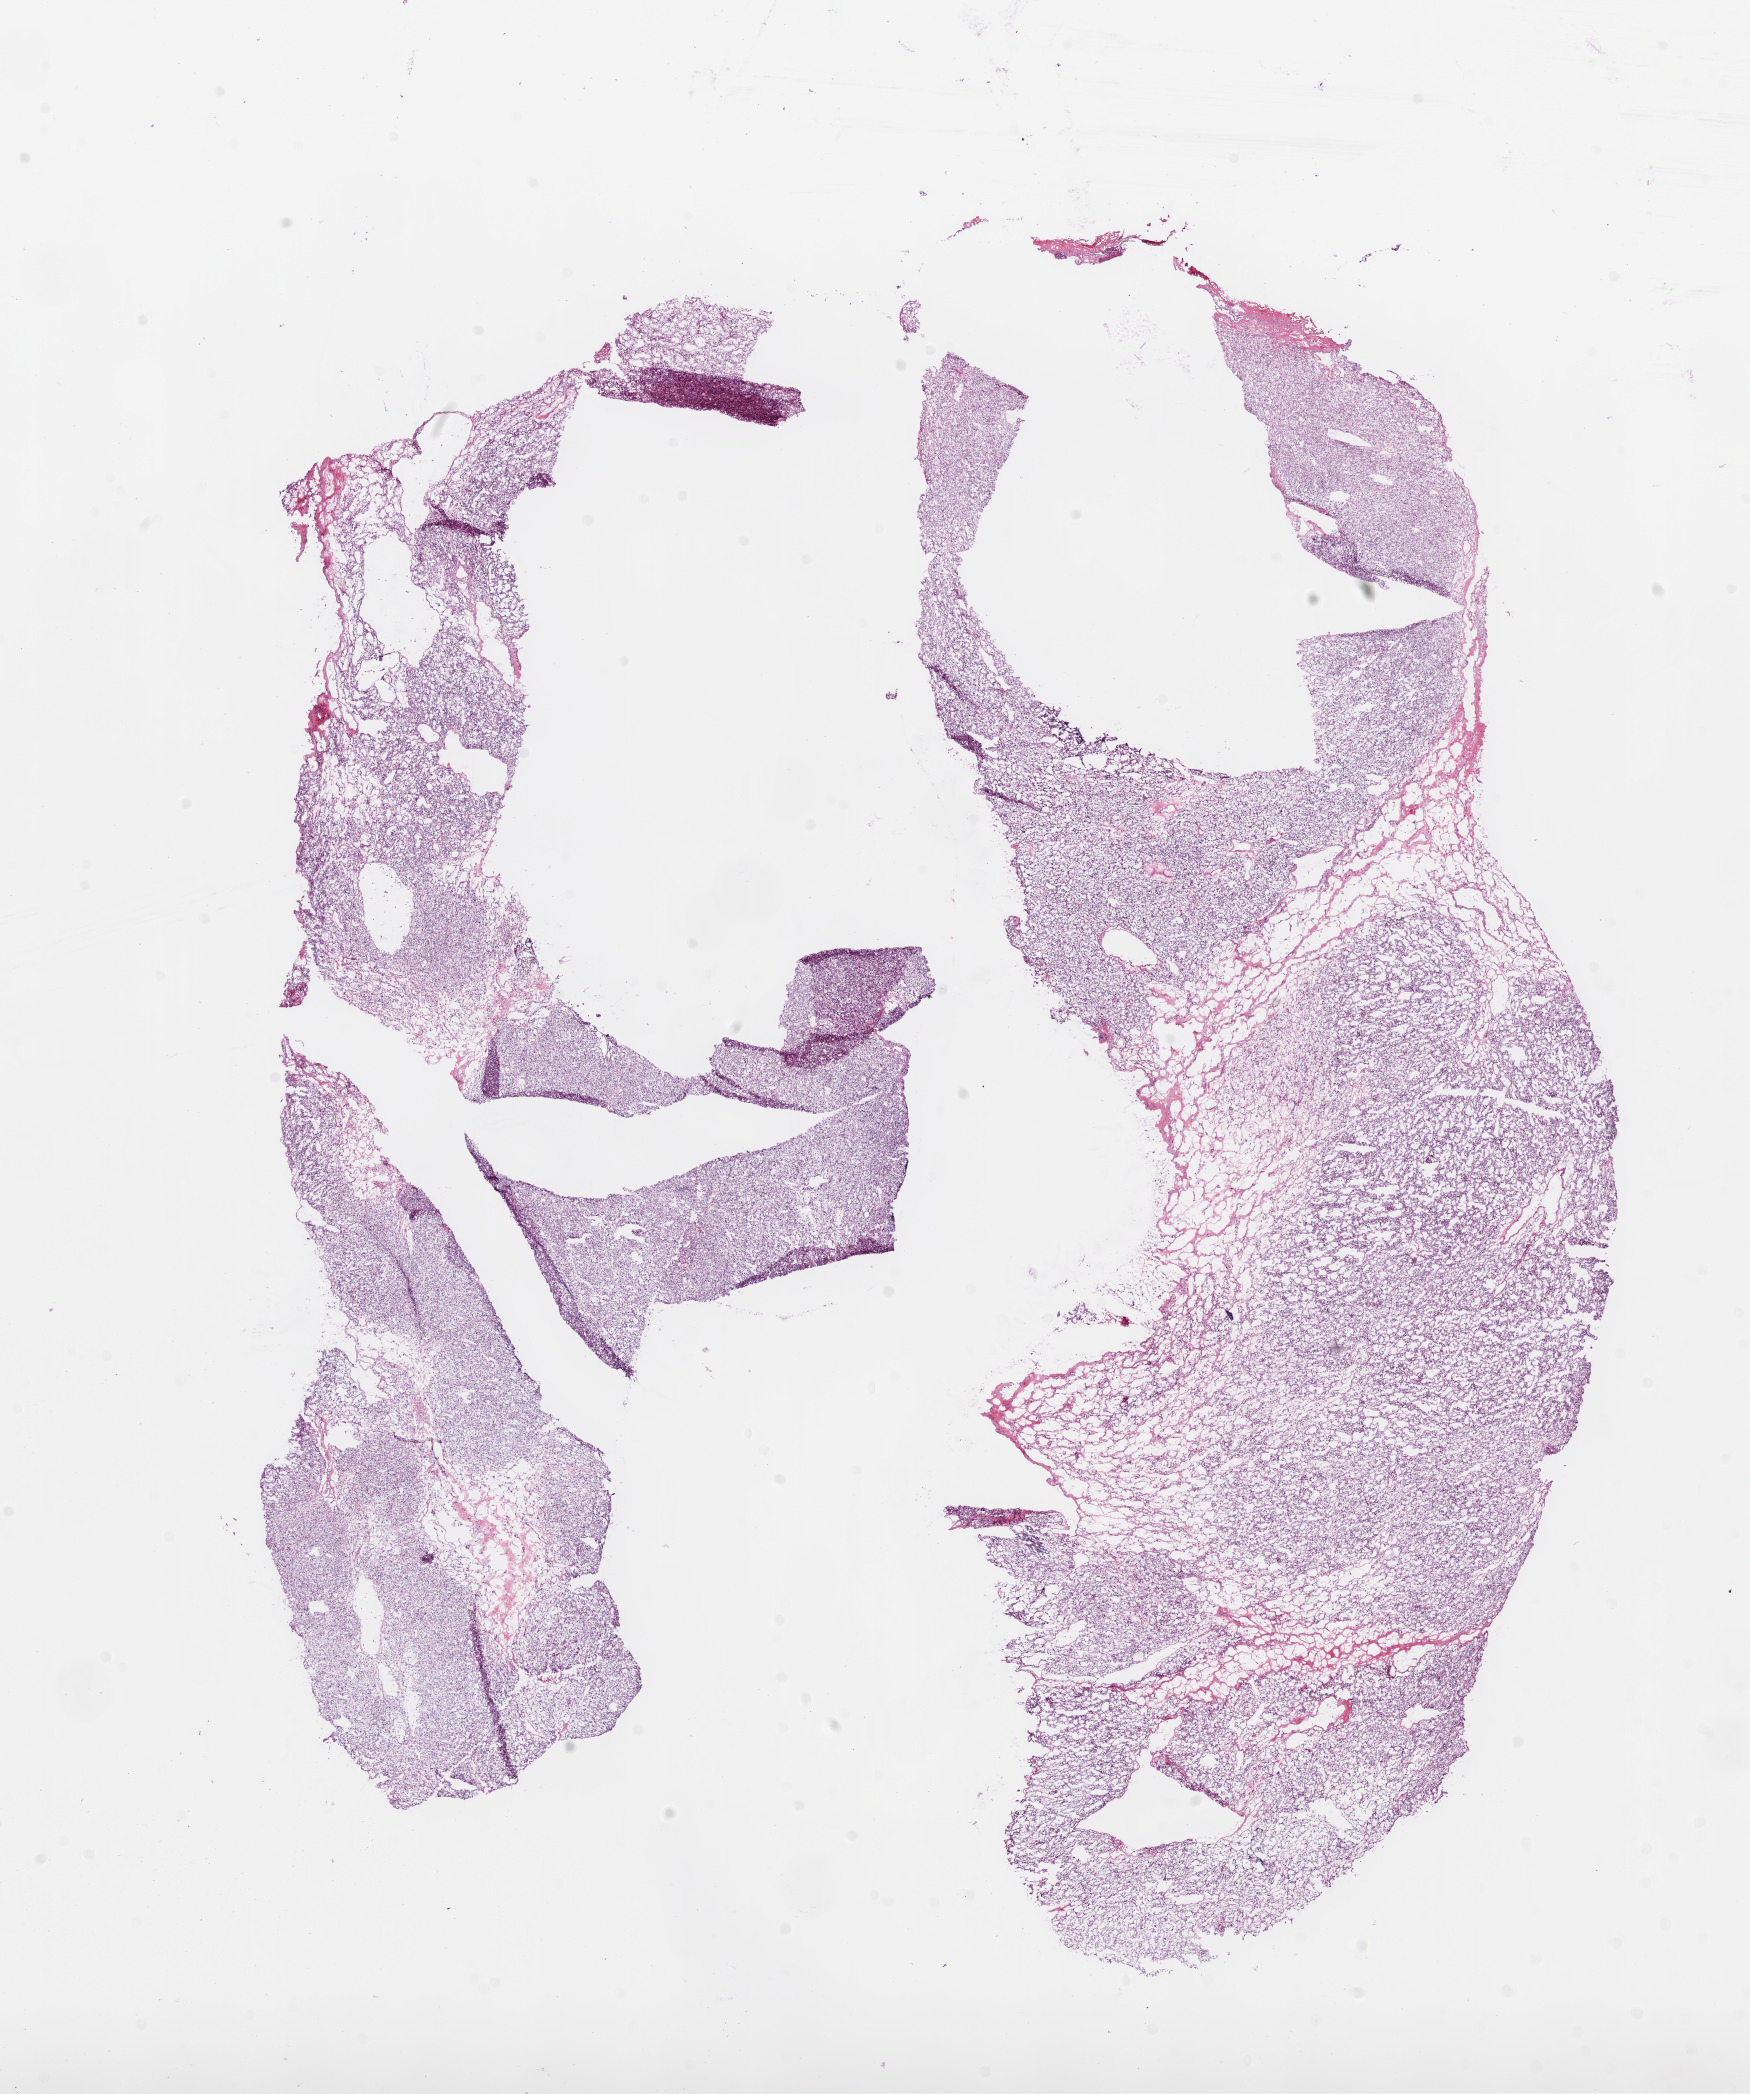
Digitized Hematoxylin and eosin (H&E) stained tissue section (whole slide), whole scanned area (about 14.0 x 16.8 mm) shown as a low-resolution overview, frozen section from the bottom of the tissue portion, primary tumour sample from the kidney. Patient sex: female. Histologic grade: G2 (moderately differentiated). Pathologist review of this section (percent, as recorded): tumour cells 85%, tumour nuclei 80%, normal cells 0%, stromal cells 15%, necrosis 0%.
AJCC pathologic stage: I (6th edition). Pathologic diagnosis: Clear cell adenocarcinoma, NOS. TNM: T1a N0 M0. Laterality: right.